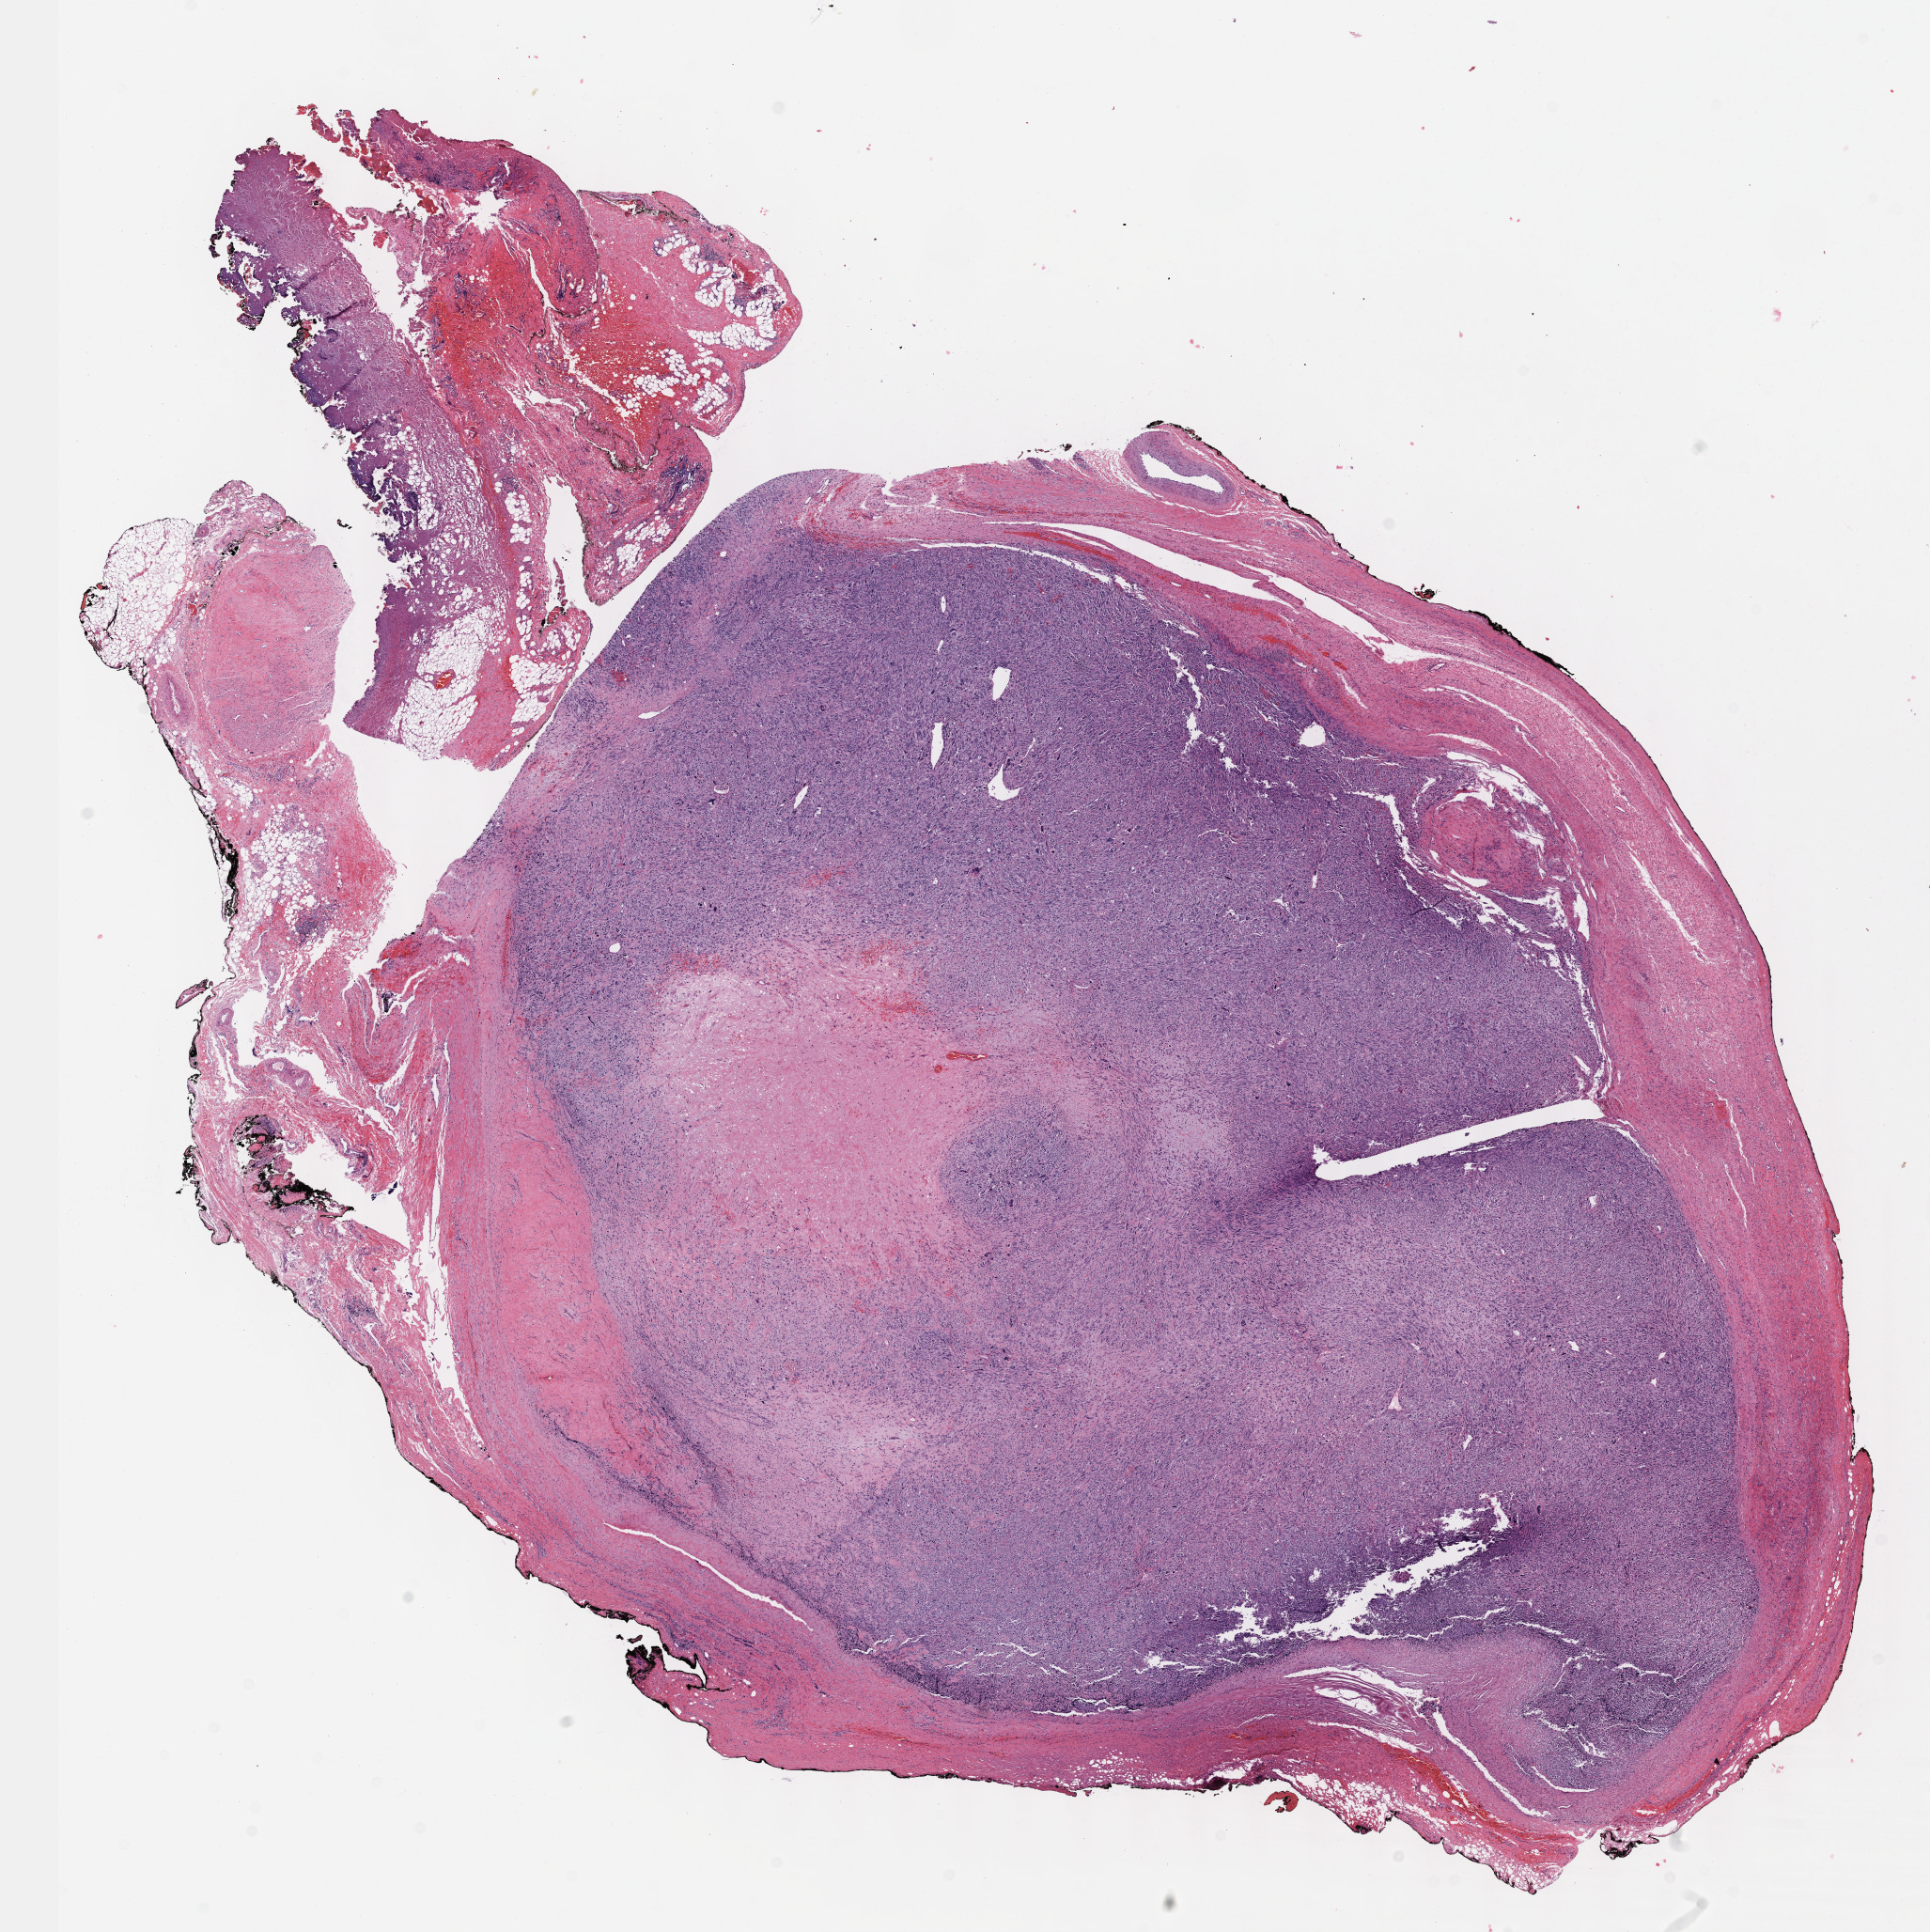
H&E whole-slide image, shown as a low-resolution overview of the whole scanned area (about 16.6 x 16.6 mm), formalin-fixed paraffin-embedded (FFPE) diagnostic section, sample: primary tumour, retroperitoneum and peritoneum. Female patient; age at initial diagnosis 31 years.
- pathologic diagnosis: Malignant peripheral nerve sheath tumor